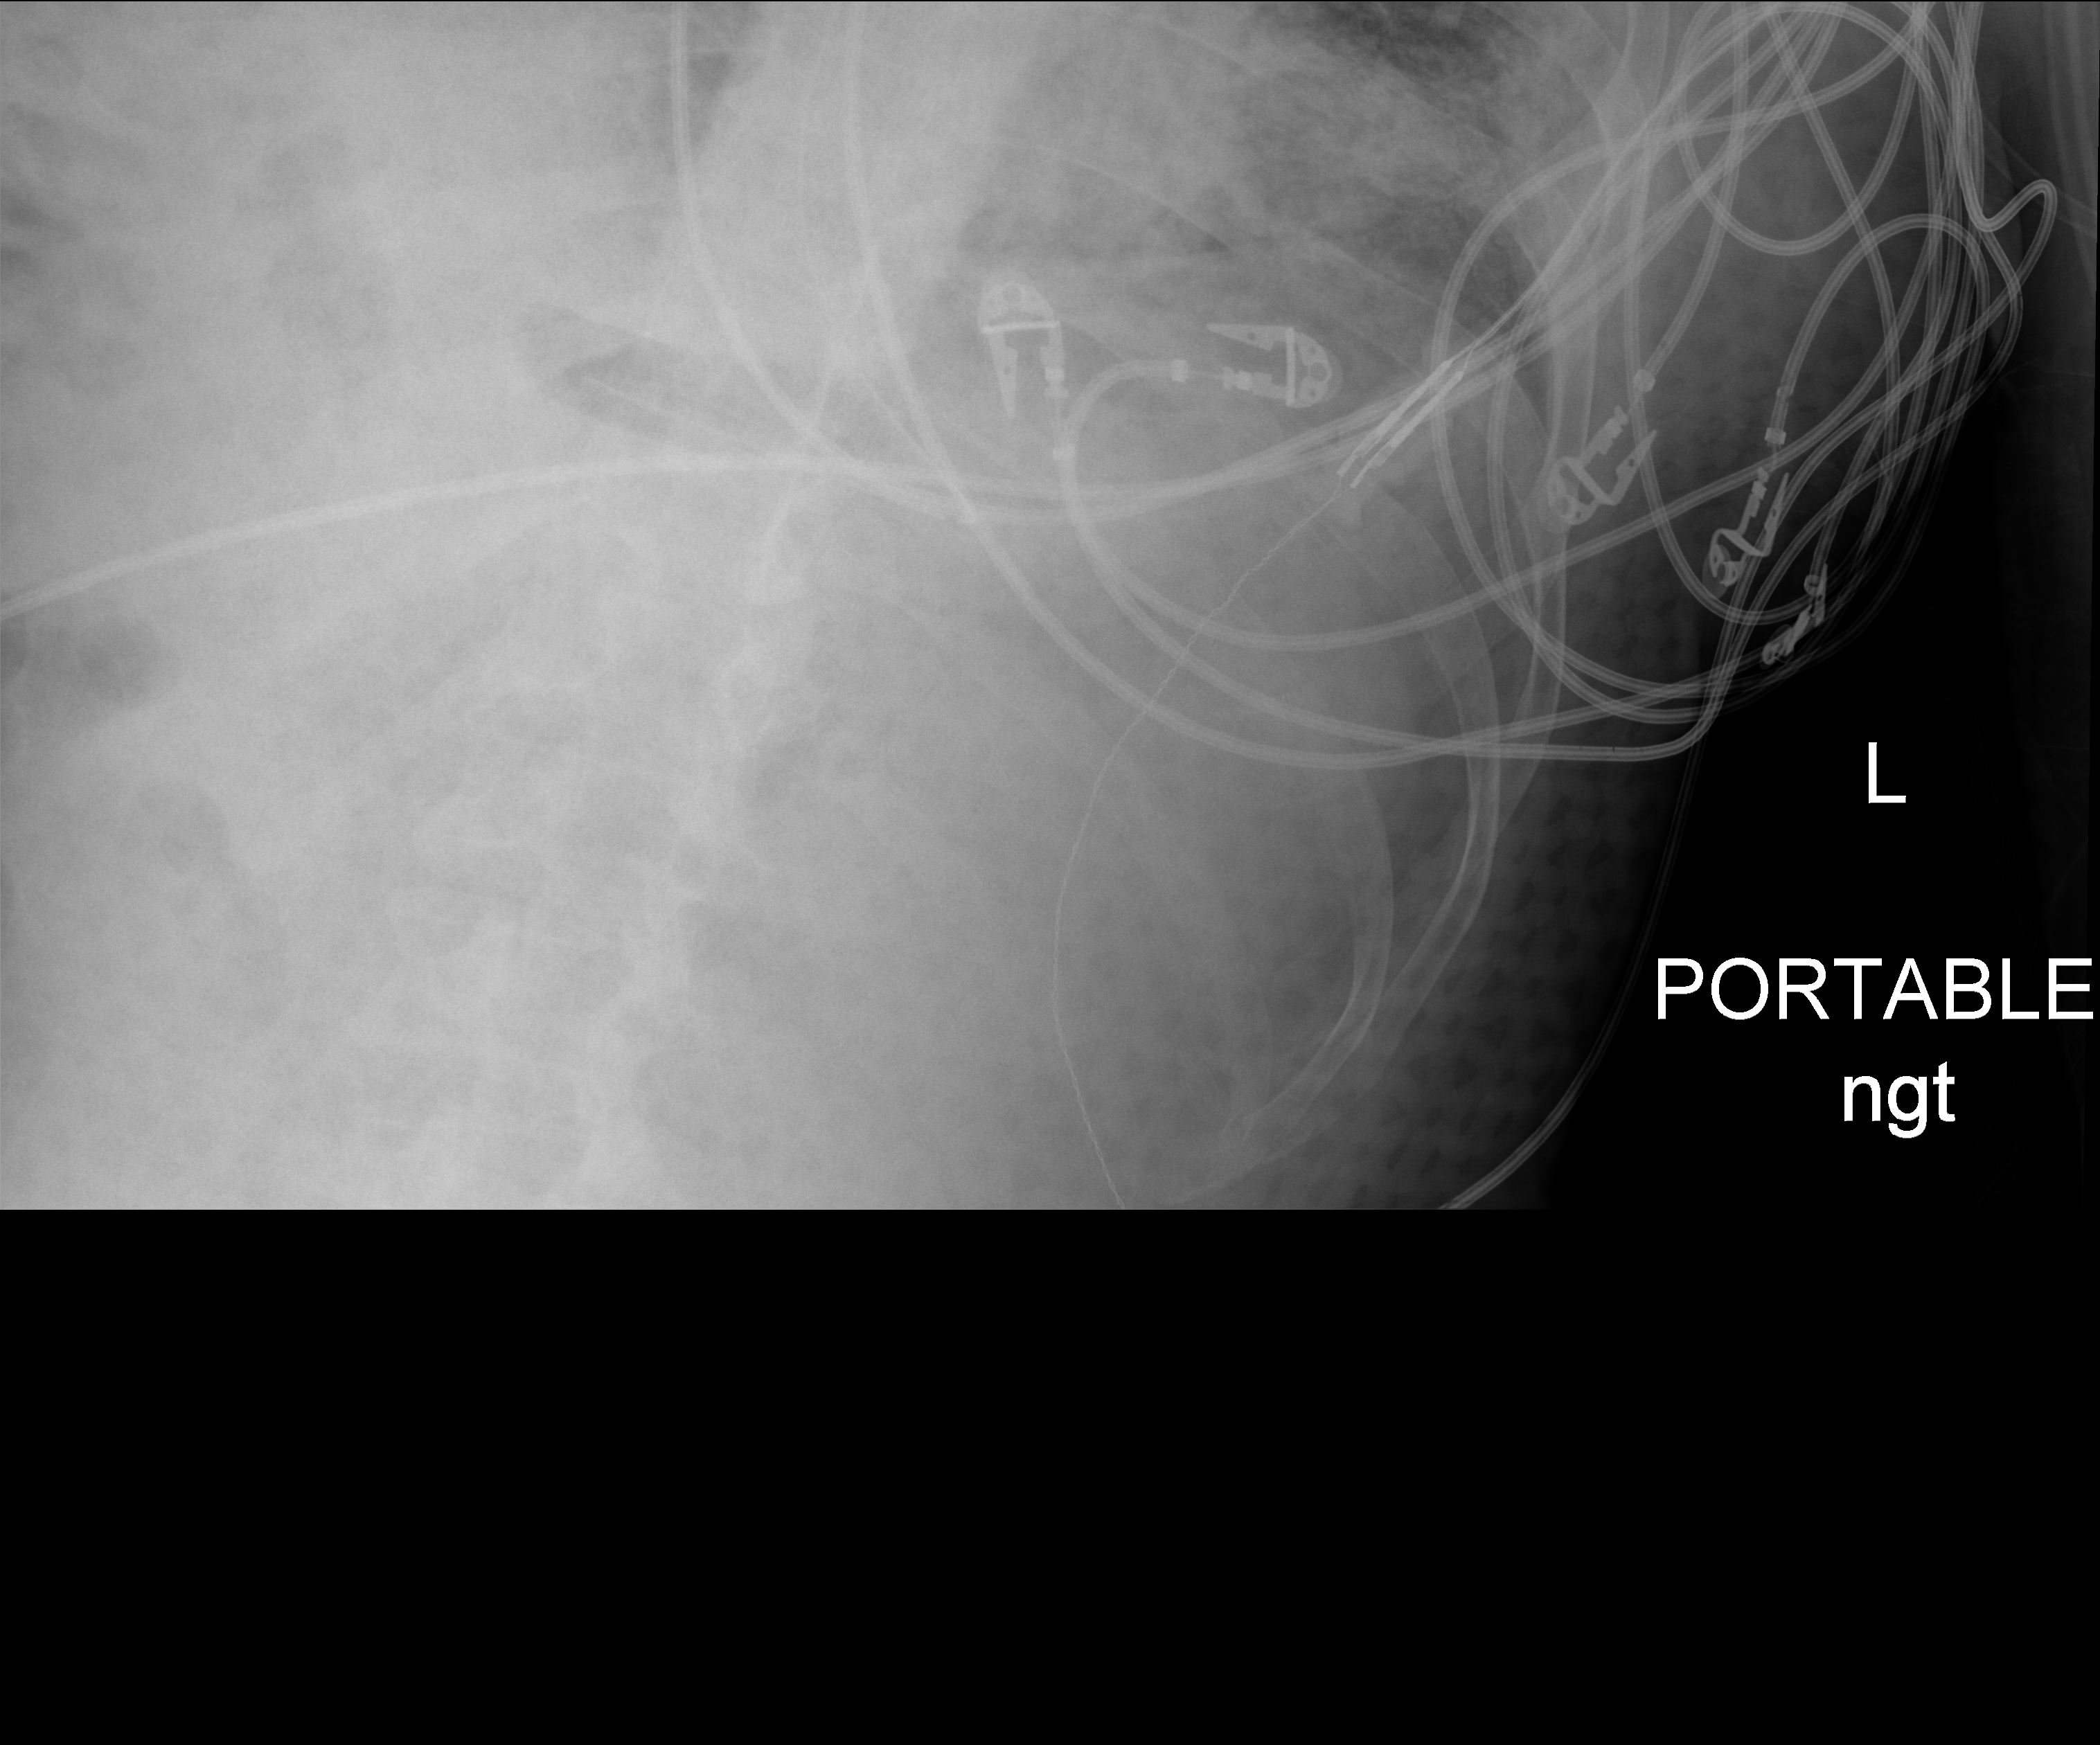
Portable chest radiograph, anteroposterior (AP) projection. Male patient hospitalised with COVID-19, age 18–59 years.
From the hospital-stay record, not from the radiograph (when in the stay this image was taken is not recorded): diabetes (admission record): no.